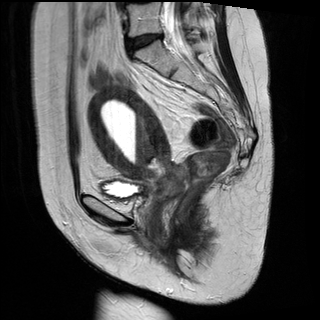
Pelvic MRI for cervical cancer, one sagittal slice; position 12 of 28 along the scan axis; T2-weighted; 1.5 T; TE 89 ms, TR 2740 ms; 320 × 320 image matrix, field of view 260 × 260 mm. Female patient, age 49 years.
Outlined on this slice (expert manual segmentation):
- uterus and cervix: bounding box [x1, y1, x2, y2] px = [87, 85, 192, 217]